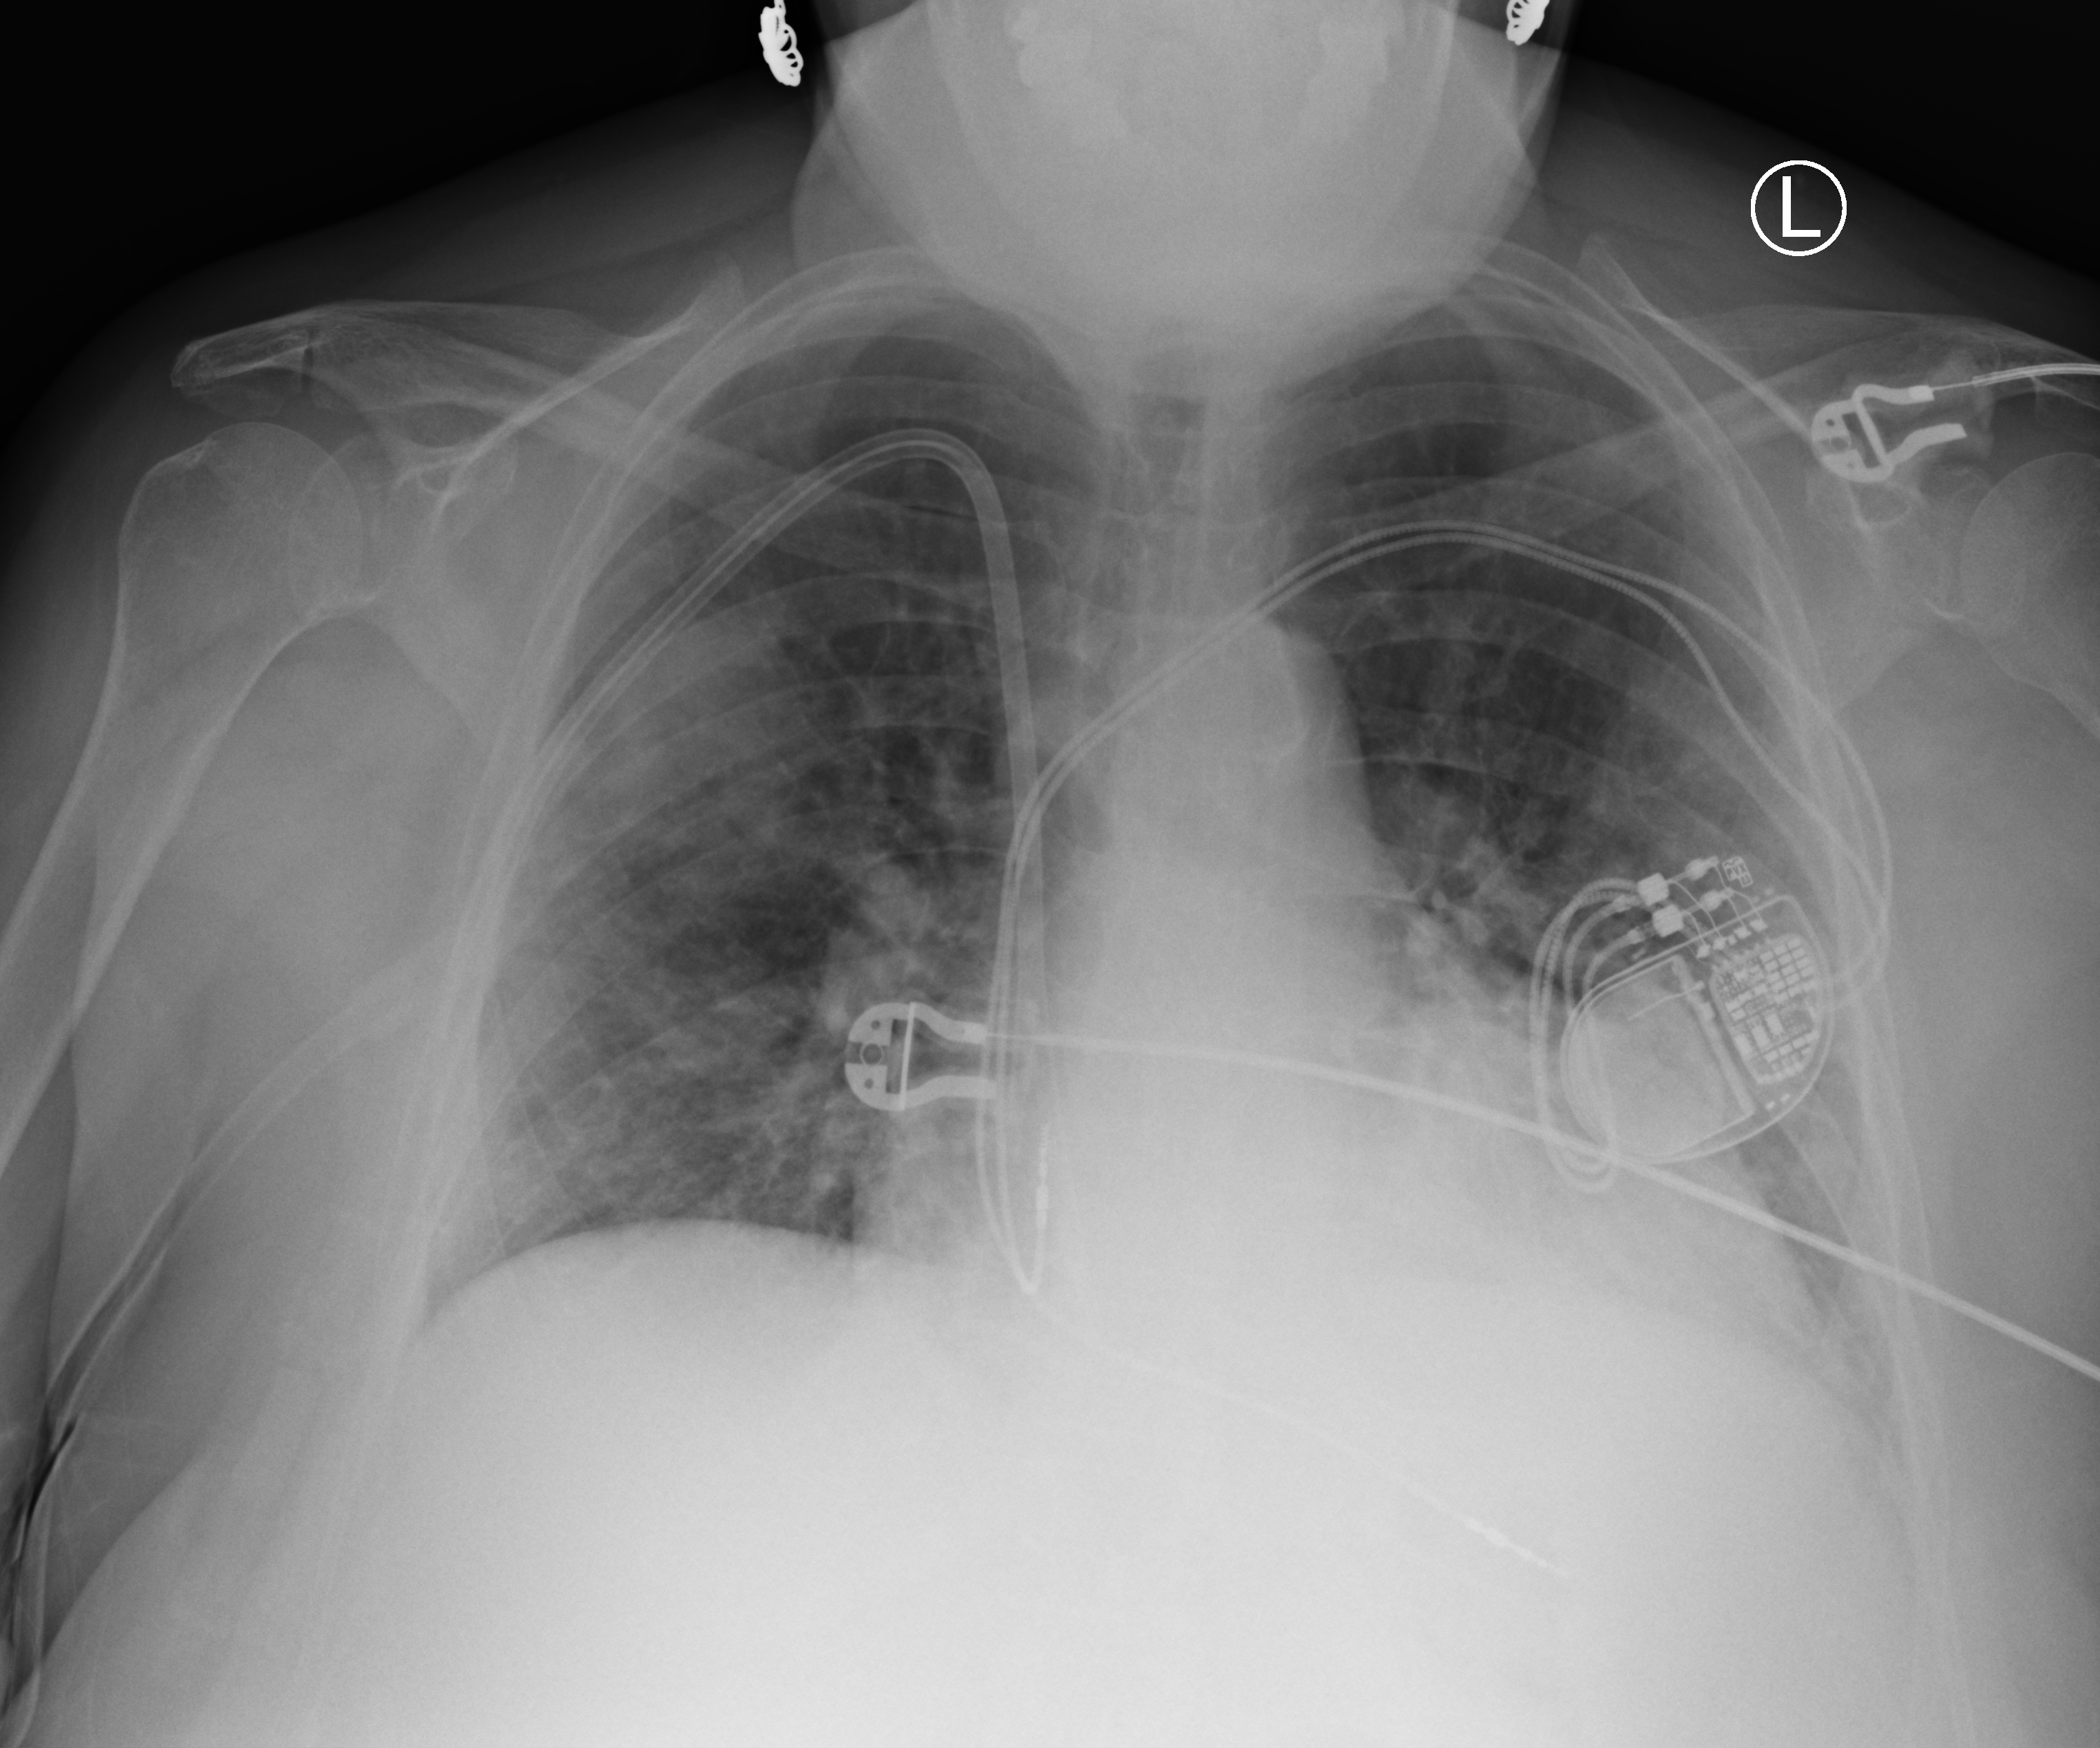
Bedside chest radiograph (computed radiography); anteroposterior (AP) projection. Female patient hospitalised with COVID-19, age 60–74 years.
From the hospital-stay record, not from the radiograph (when in the stay this image was taken is not recorded): admitted to intensive care during this hospital stay: no.